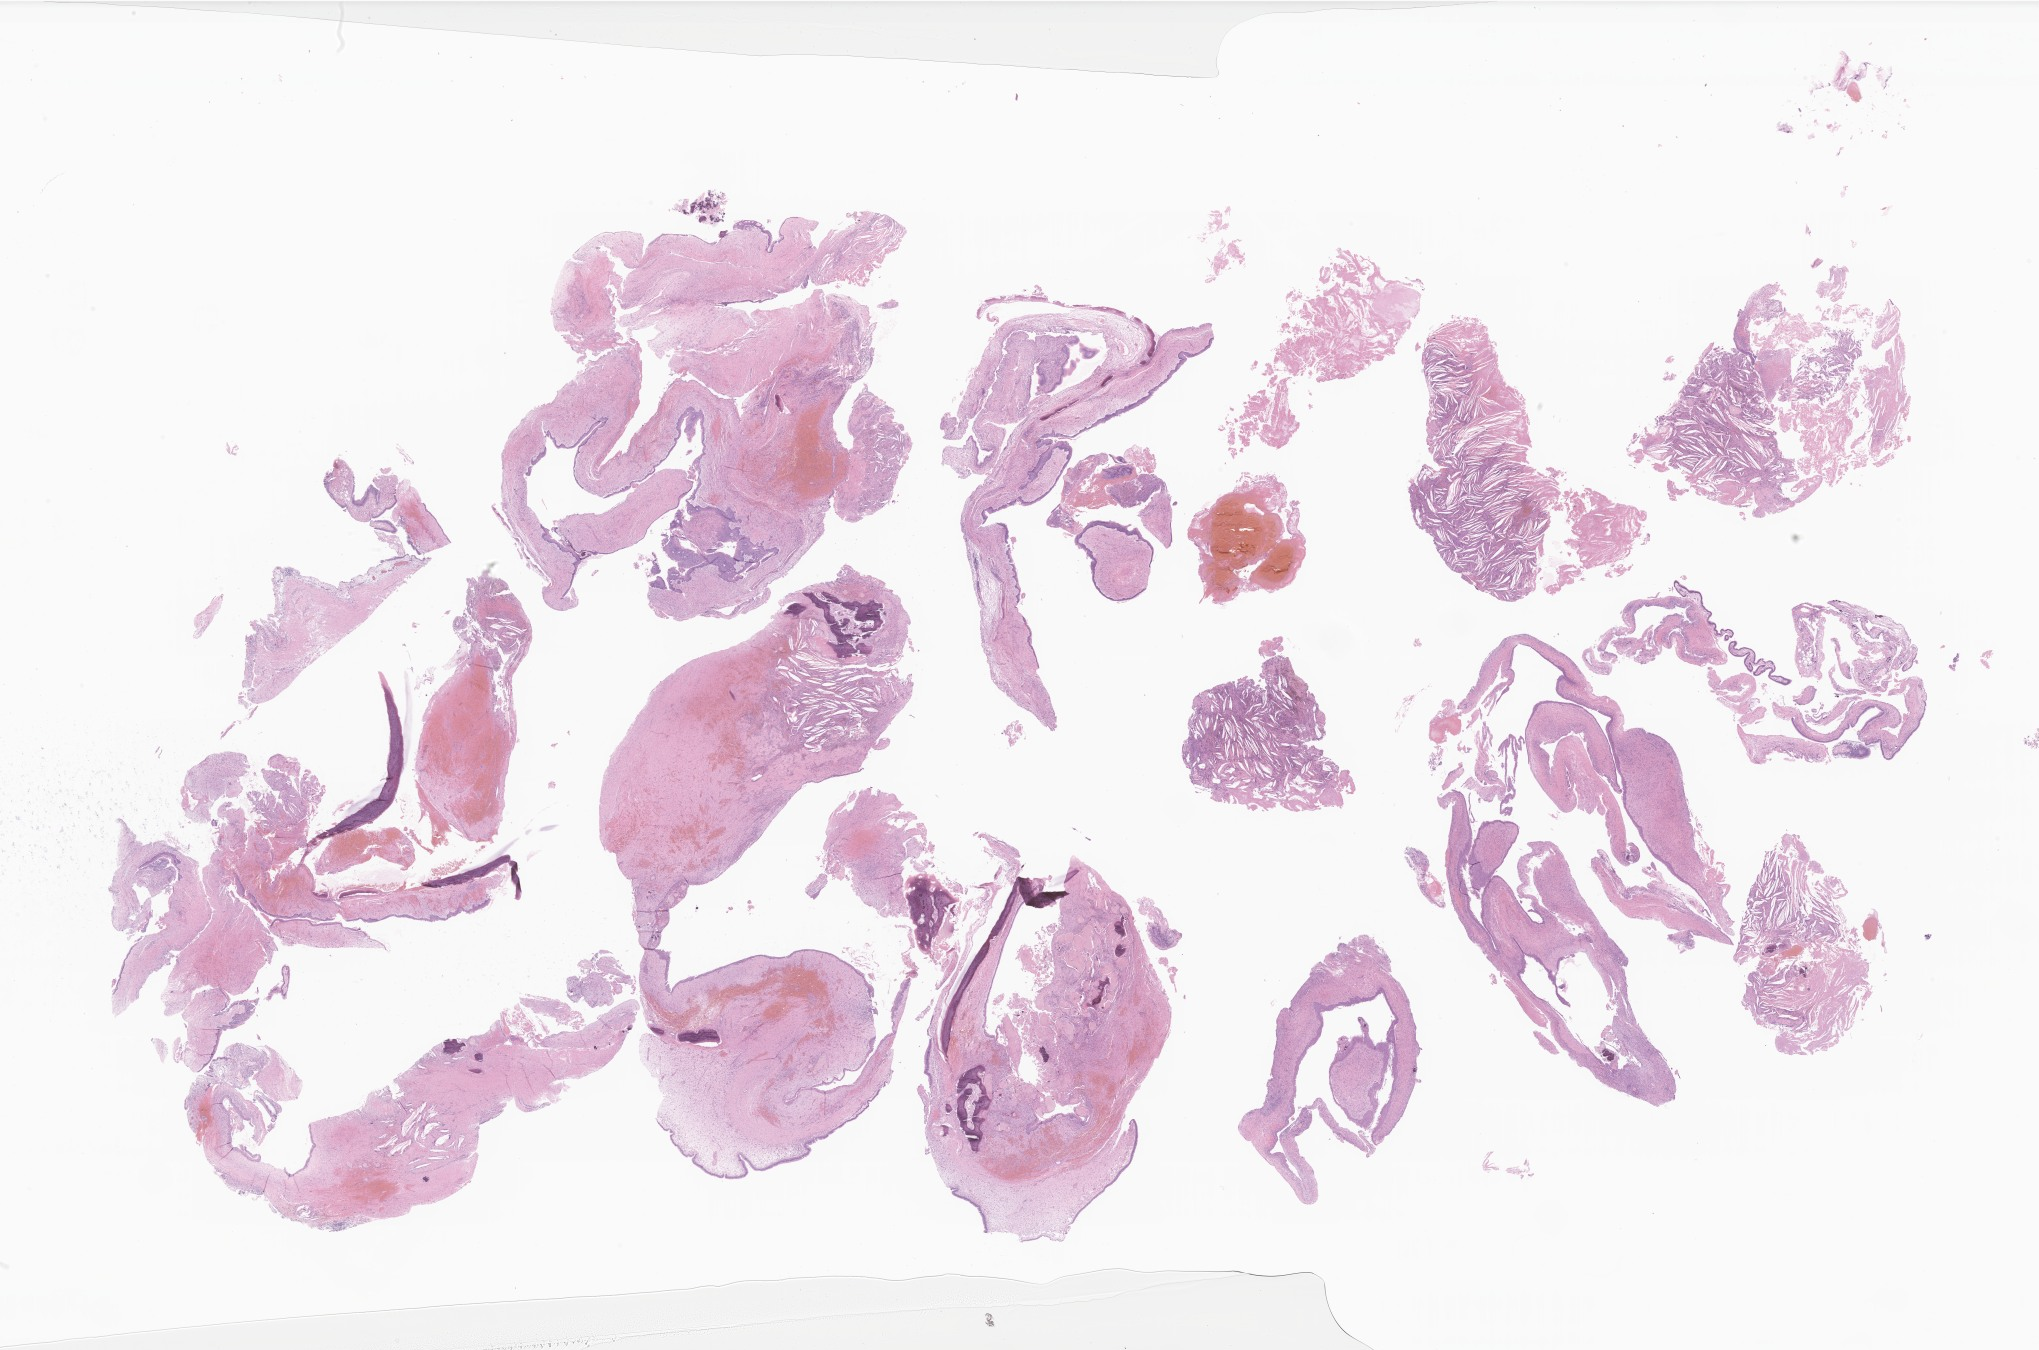
Digitized hematoxylin and eosin (H&E)-stained section of tumor tissue from the brain — whole scanned area (about 34.4 x 22.8 mm) shown as a low-resolution overview. Formalin-fixed paraffin-embedded section. Patient male; age 163 months (13 years 7 months).
Diagnosis (ICD-O-3 morphology term): Craniopharyngioma, adamantinomatous.